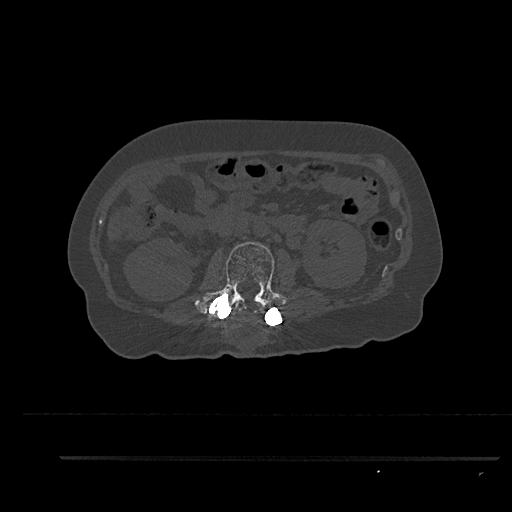
CT including the spine, one axial slice; position 159 of 797 along the scan axis; reconstruction kernel Br40s/3; bone window (W 1800 / L 400 HU); 0.5 mm slice thickness; 512 × 512 image matrix, field of view 408 × 408 mm. Female patient, age 44 years. From the clinical record (not read from this slice): primary cancer: renal.
Outlined on this slice (semi-automatic segmentation, software-assisted and operator-edited):
- L2 vertebra: bounding box <195,242,285,320> (left, top, right, bottom; pixels)